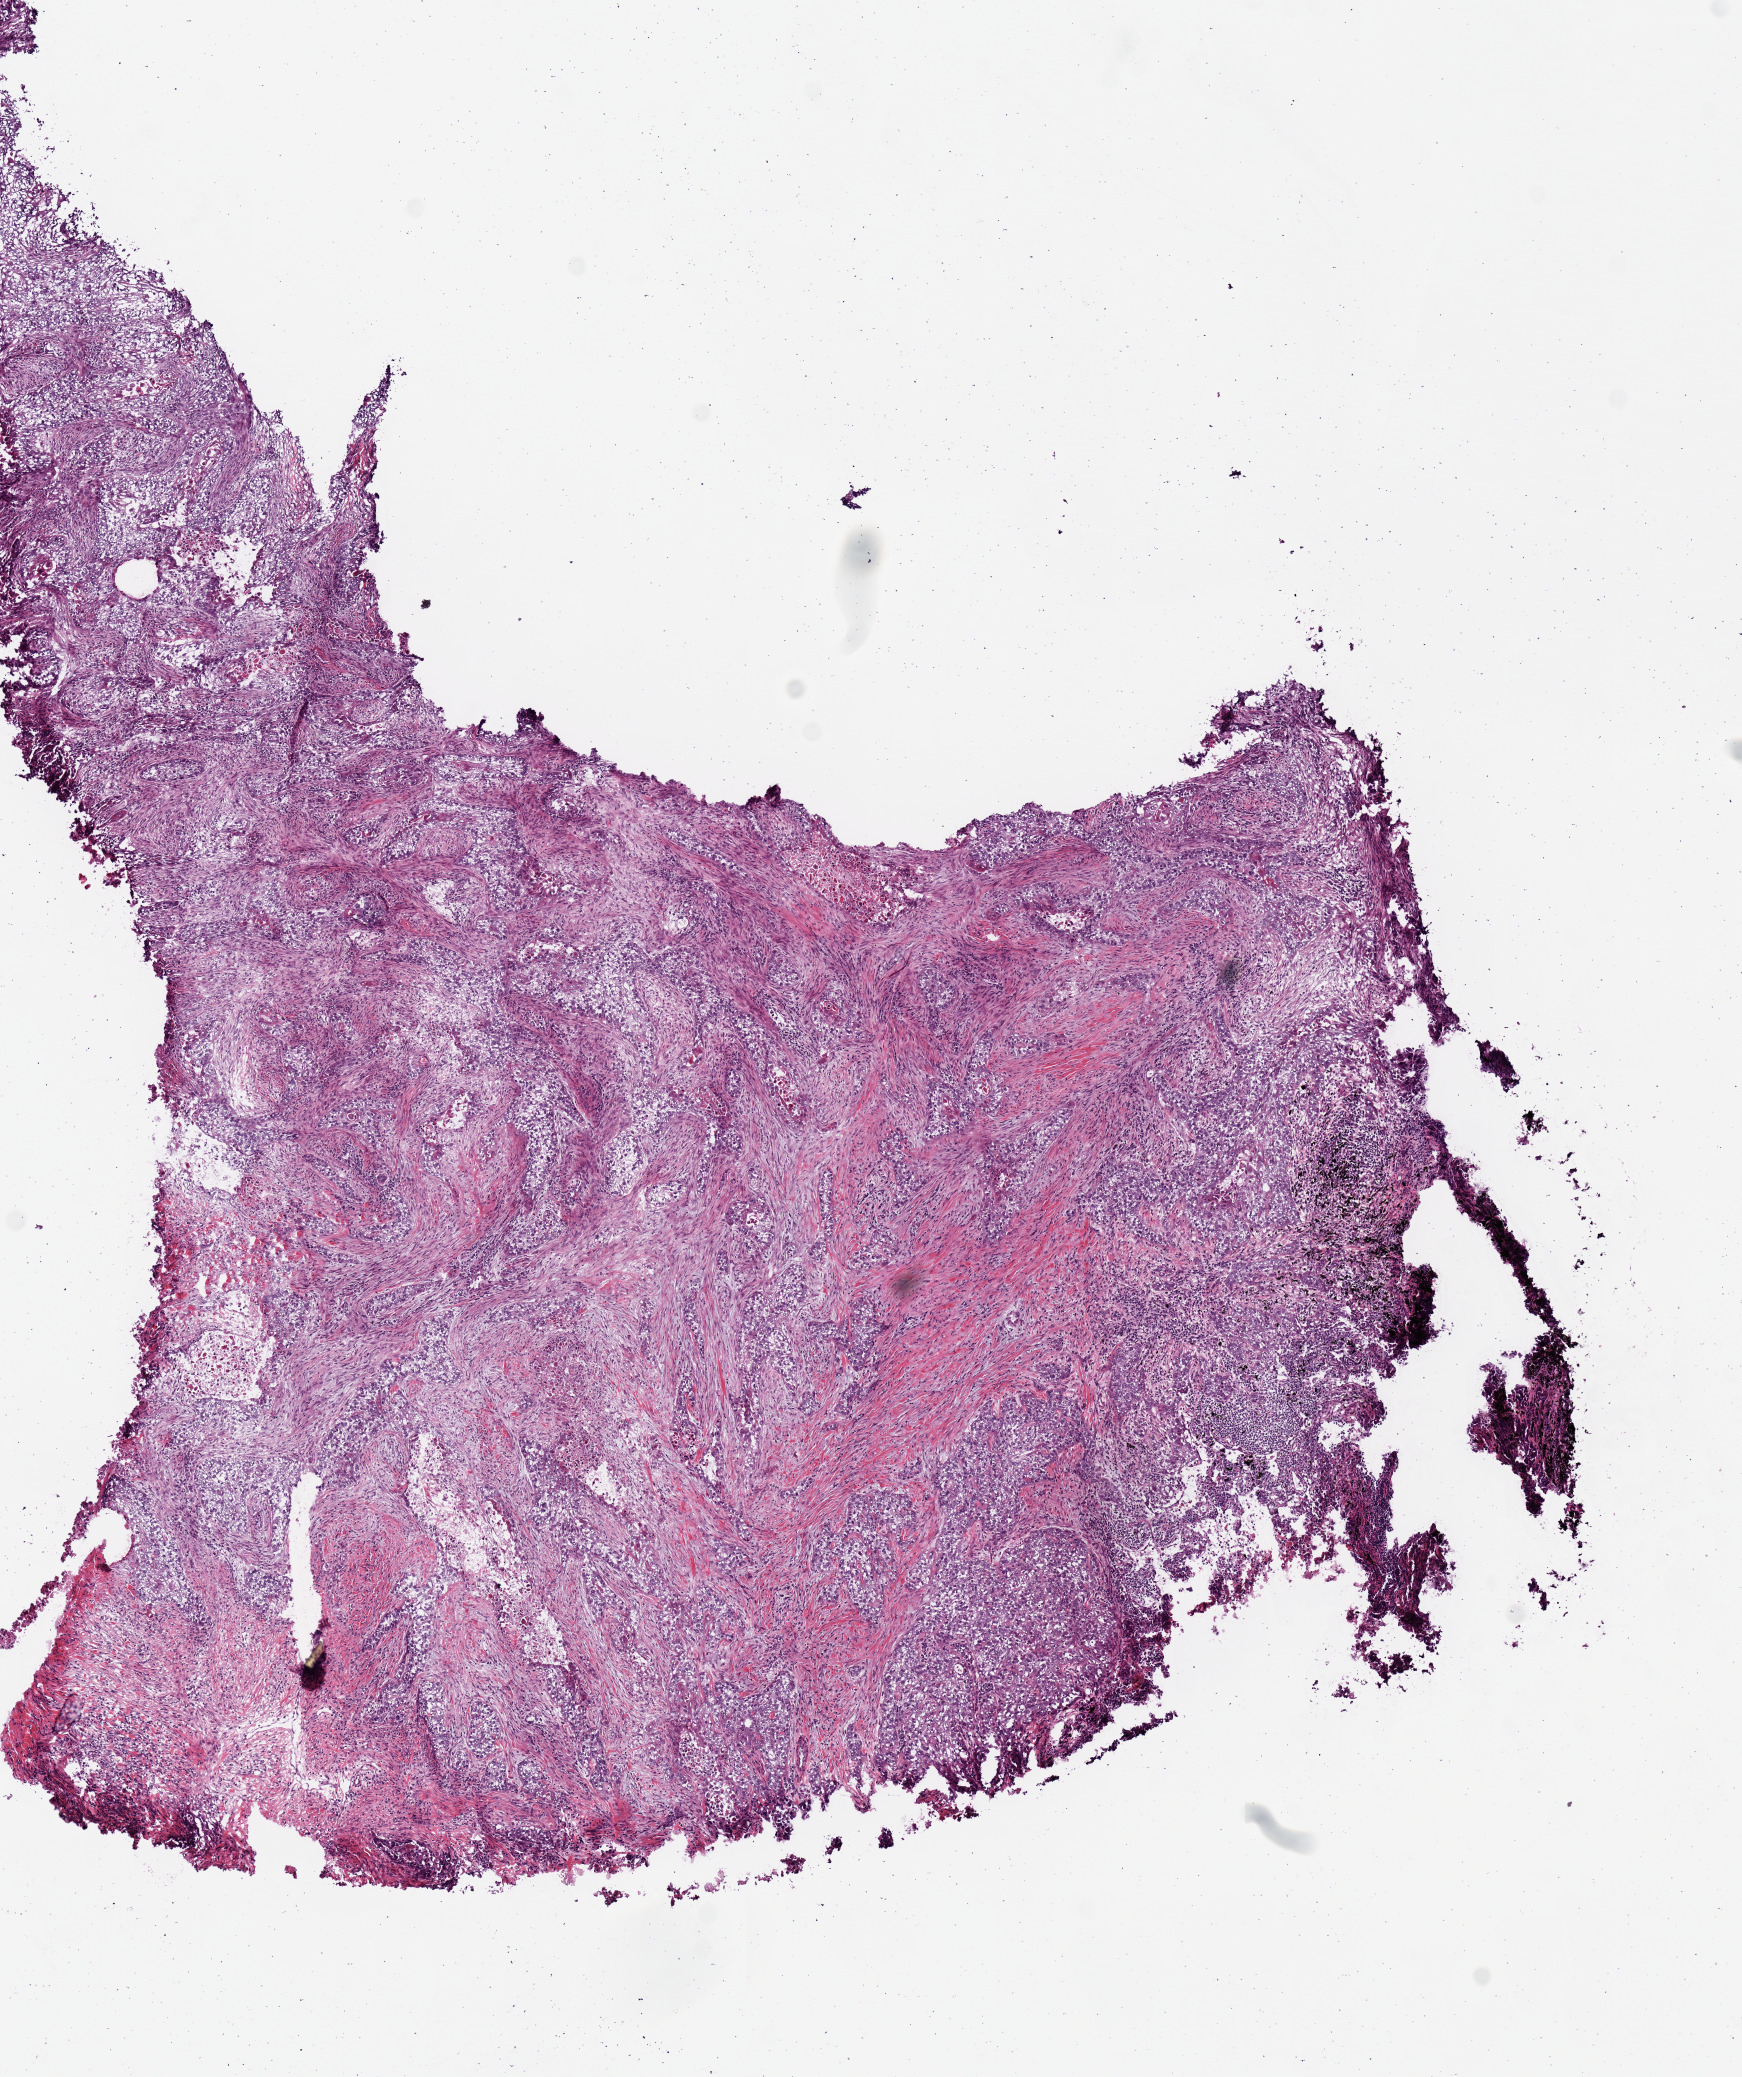
Whole-slide histology image, Hematoxylin and eosin (H&E) stained — a low-resolution overview of the entire scanned area, about 6.9 x 8.2 mm. Frozen section from the bottom of the tissue portion. Lung, primary tumour sample. Male, age 73 years at initial diagnosis.
Histologic diagnosis: Squamous cell carcinoma, NOS.